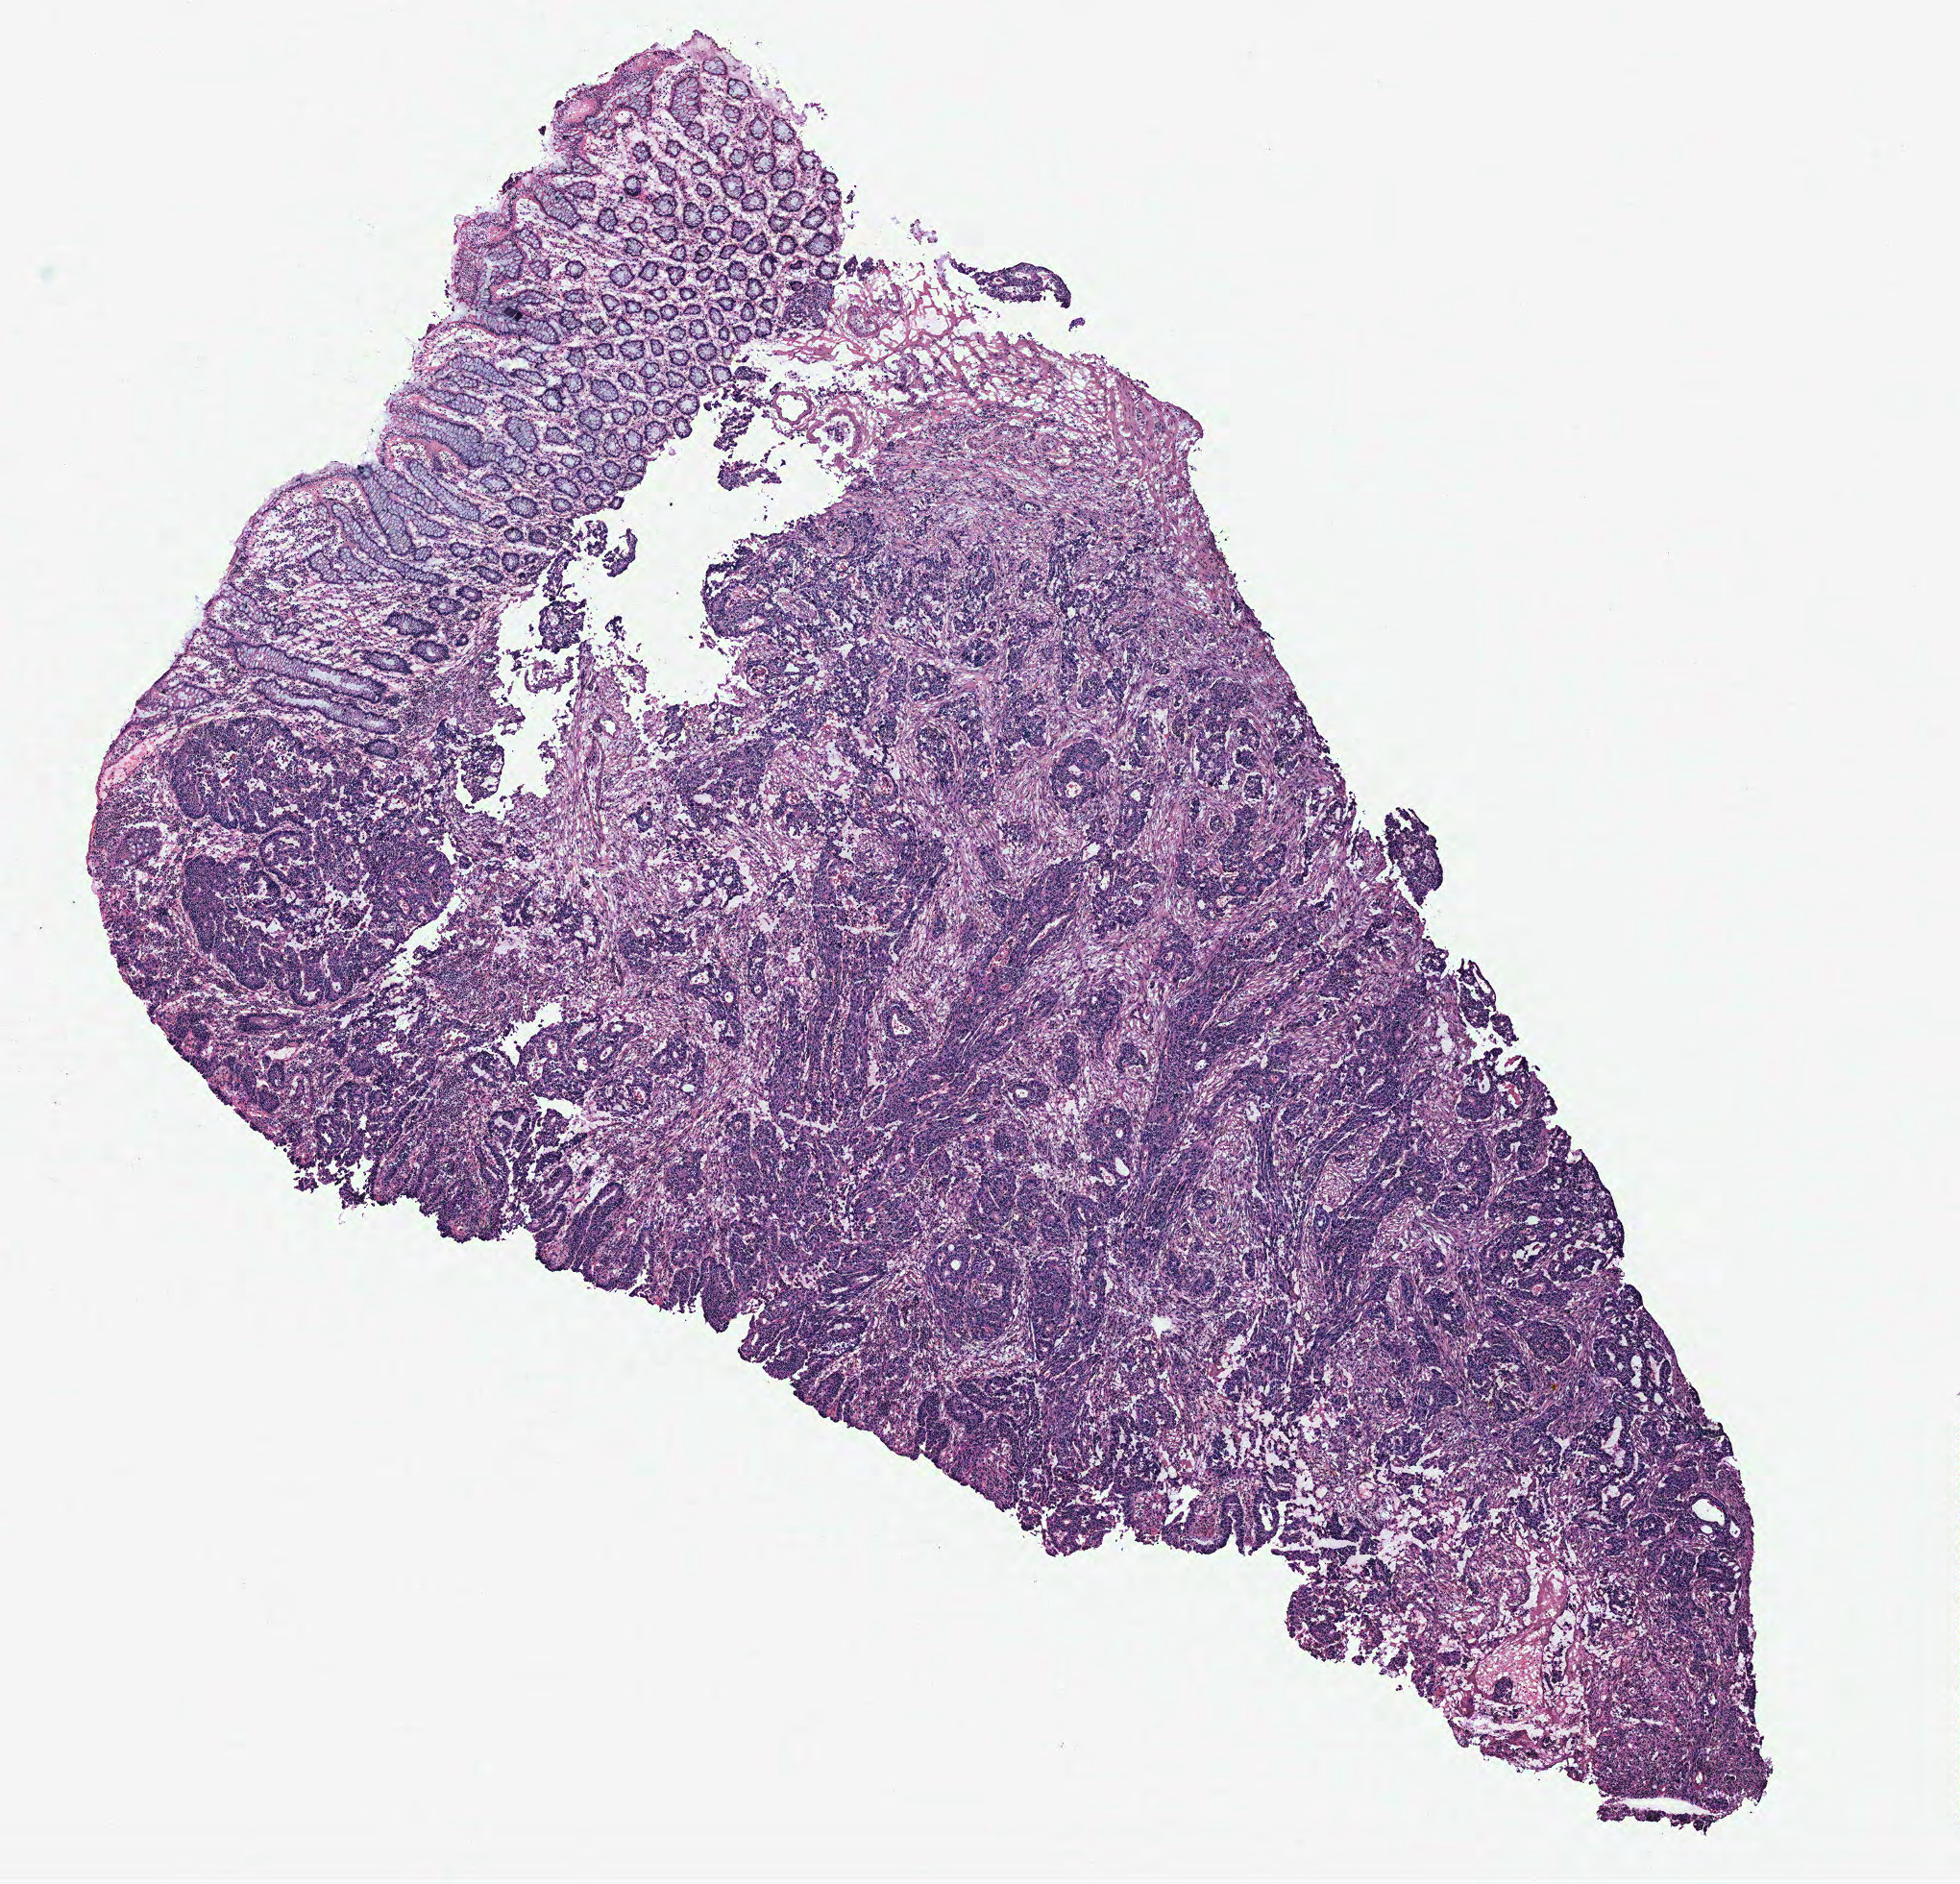
Hematoxylin and eosin (H&E) stained whole-slide image — a low-resolution overview of the entire scanned area, about 8.2 x 7.8 mm, colon, tissue type not recorded.
Patient diagnosis (cohort enrolment): colon cancer (colon).